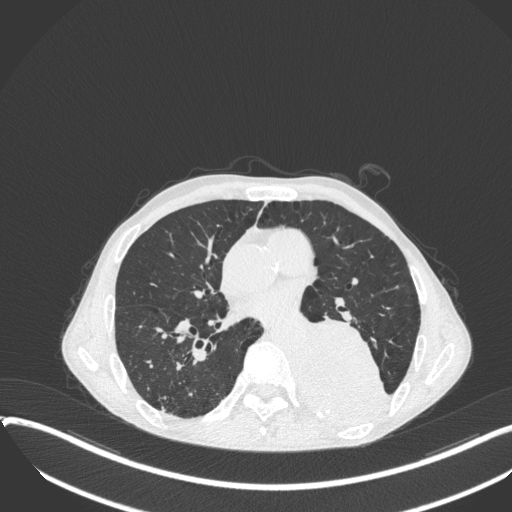
Chest CT, one axial slice. Position 177 of 400 along the scan axis. Lung window (W 1500 / L -600 HU). 1 mm slice thickness. 512 × 512 image matrix. Male patient, age 57 years. Case-level facts recorded for this patient, not image findings: clinical TNM (as recorded): T4 N0 M0.
Annotated regions visible in this slice (rectangle marked by the reading radiologist):
- lung tumour (recorded histology: squamous cell carcinoma): box from (x=298, y=311) to (x=397, y=422) px